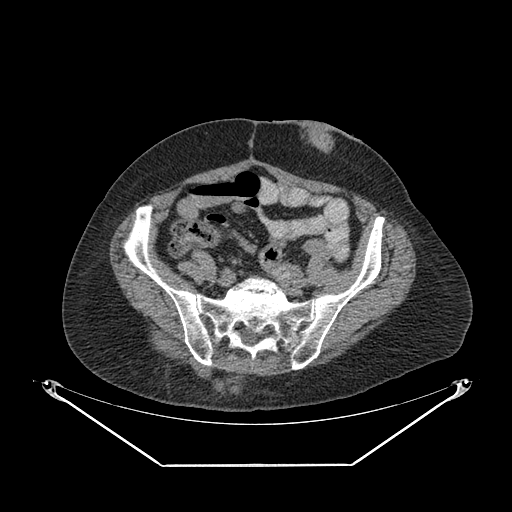
CT of an extremity soft-tissue mass (from a PET/CT study), one axial slice. Position 77 of 267 along the scan axis. 140 kVp. Soft-tissue window (W 400 / L 40 HU). 3.75 mm slice thickness. 512 × 512 image matrix. Female patient. Case-level facts recorded for this patient, not image findings: histological type: spindle cell suggestive of myxofibrosarcoma; grade: intermediate; site of the primary tumour: right buttock.
Outlined on this slice (expert contour drawn on MRI and transferred to this co-registered scan by the dataset authors):
- gross tumour volume (mass): bounding box [x1, y1, x2, y2] px = [176, 352, 247, 396]